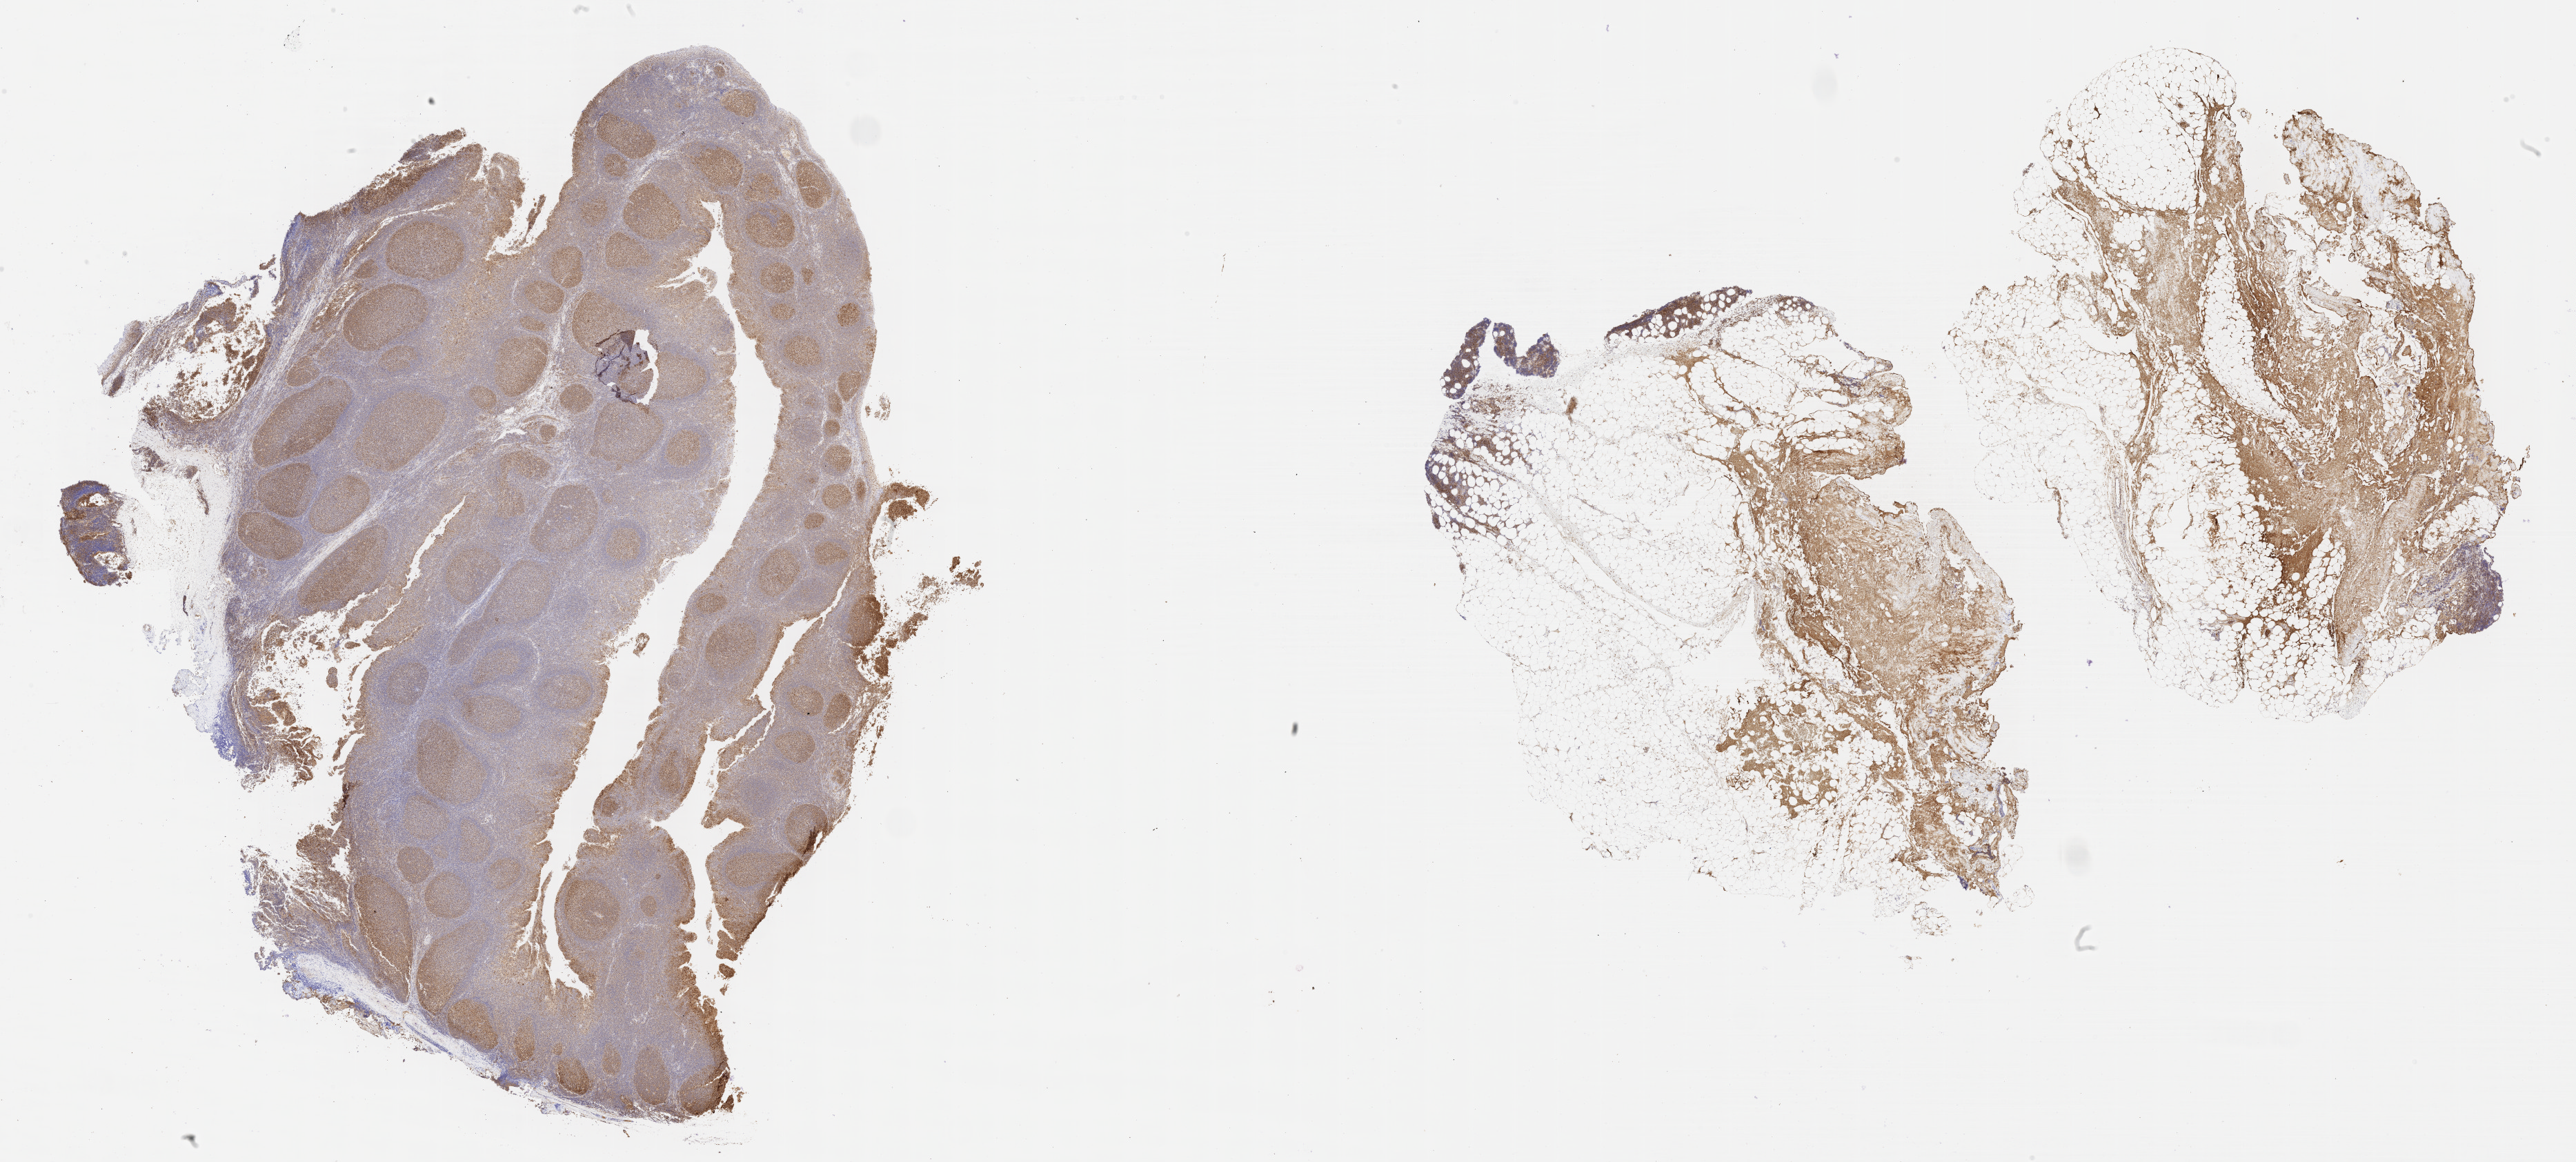
Whole-slide image, immunohistochemical stain for BCL6 — shown as a low-resolution overview of the whole scanned area (about 30.2 x 13.6 mm); tumor tissue; site: upper limb lymph node. Patient: male, age 76 years.
Histologic diagnosis: Burkitt lymphoma, NOS.